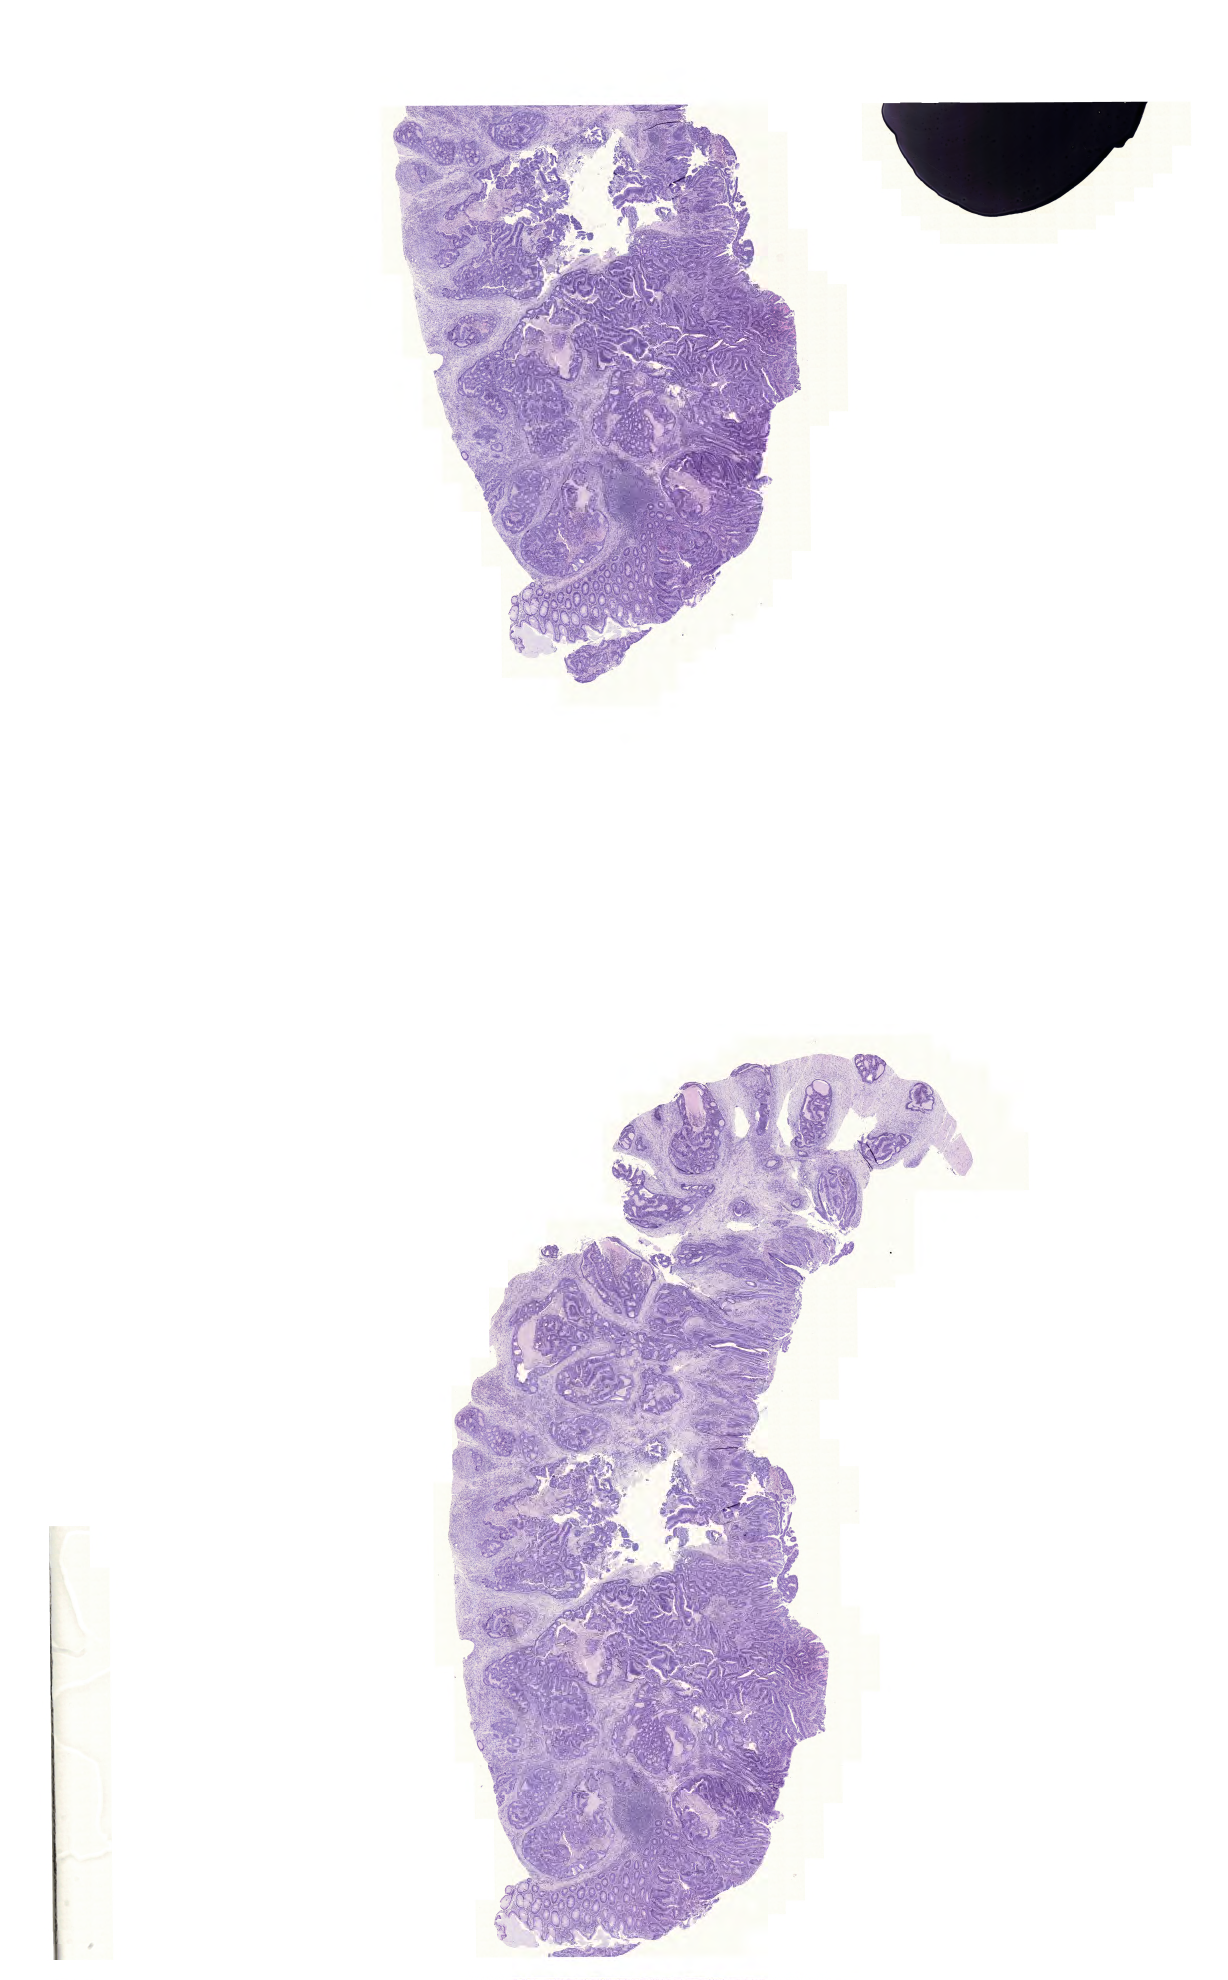
Hematoxylin and eosin (H&E) stained whole-slide image — a low-resolution overview of the entire scanned area, about 18.3 x 29.5 mm, formalin-fixed paraffin-embedded (FFPE) diagnostic section, primary tumour sample from the colon. Male, age 59 years at initial diagnosis.
AJCC pathologic stage: IIA (6th edition). Diagnosis: Adenocarcinoma, NOS. Lymph nodes positive (case pathology): 0 of 13 examined.